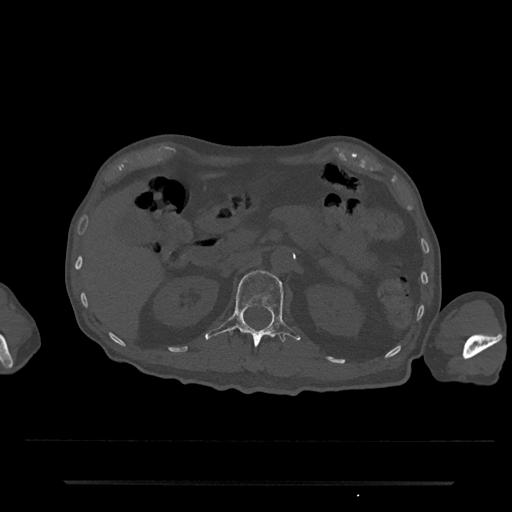
CT including the spine, one axial slice; position 133 of 797 along the scan axis; reconstruction kernel Br40s/3; 120 kVp; bone window (W 1800 / L 400 HU); 0.5 mm slice thickness; 512 × 512 image matrix. Patient: male, 74 years. From the clinical record (not read from this slice): primary cancer: prostate.
Structures marked on this image (semi-automatically segmented with operator editing):
- L1 vertebra: bounding box (x1, y1, x2, y2) in pixels: (205, 271, 301, 346)